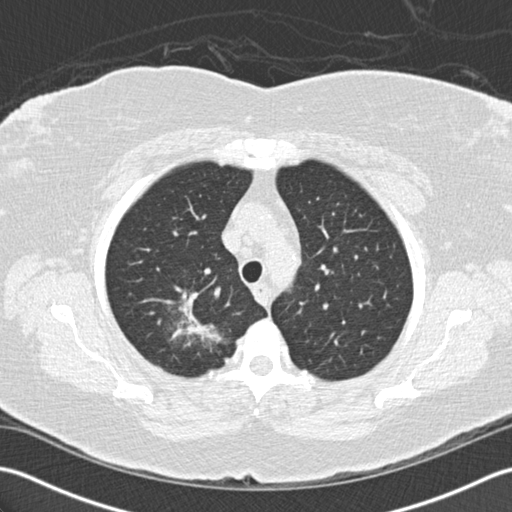
Chest CT (low-dose screening protocol), one axial image. Baseline annual screen. Lung window (W 1500 / L -600 HU). 2 mm slice thickness. 120 kVp. Slice 30 of 156 in the series. Female participant, aged 72 years at enrolment.
- Expert-annotated lung lesion, box from (x=138, y=274) to (x=234, y=368) px.
- The screening reader recorded 2 non-calcified nodules or masses ≥4 mm on this exam; which of them this box marks is not recorded.